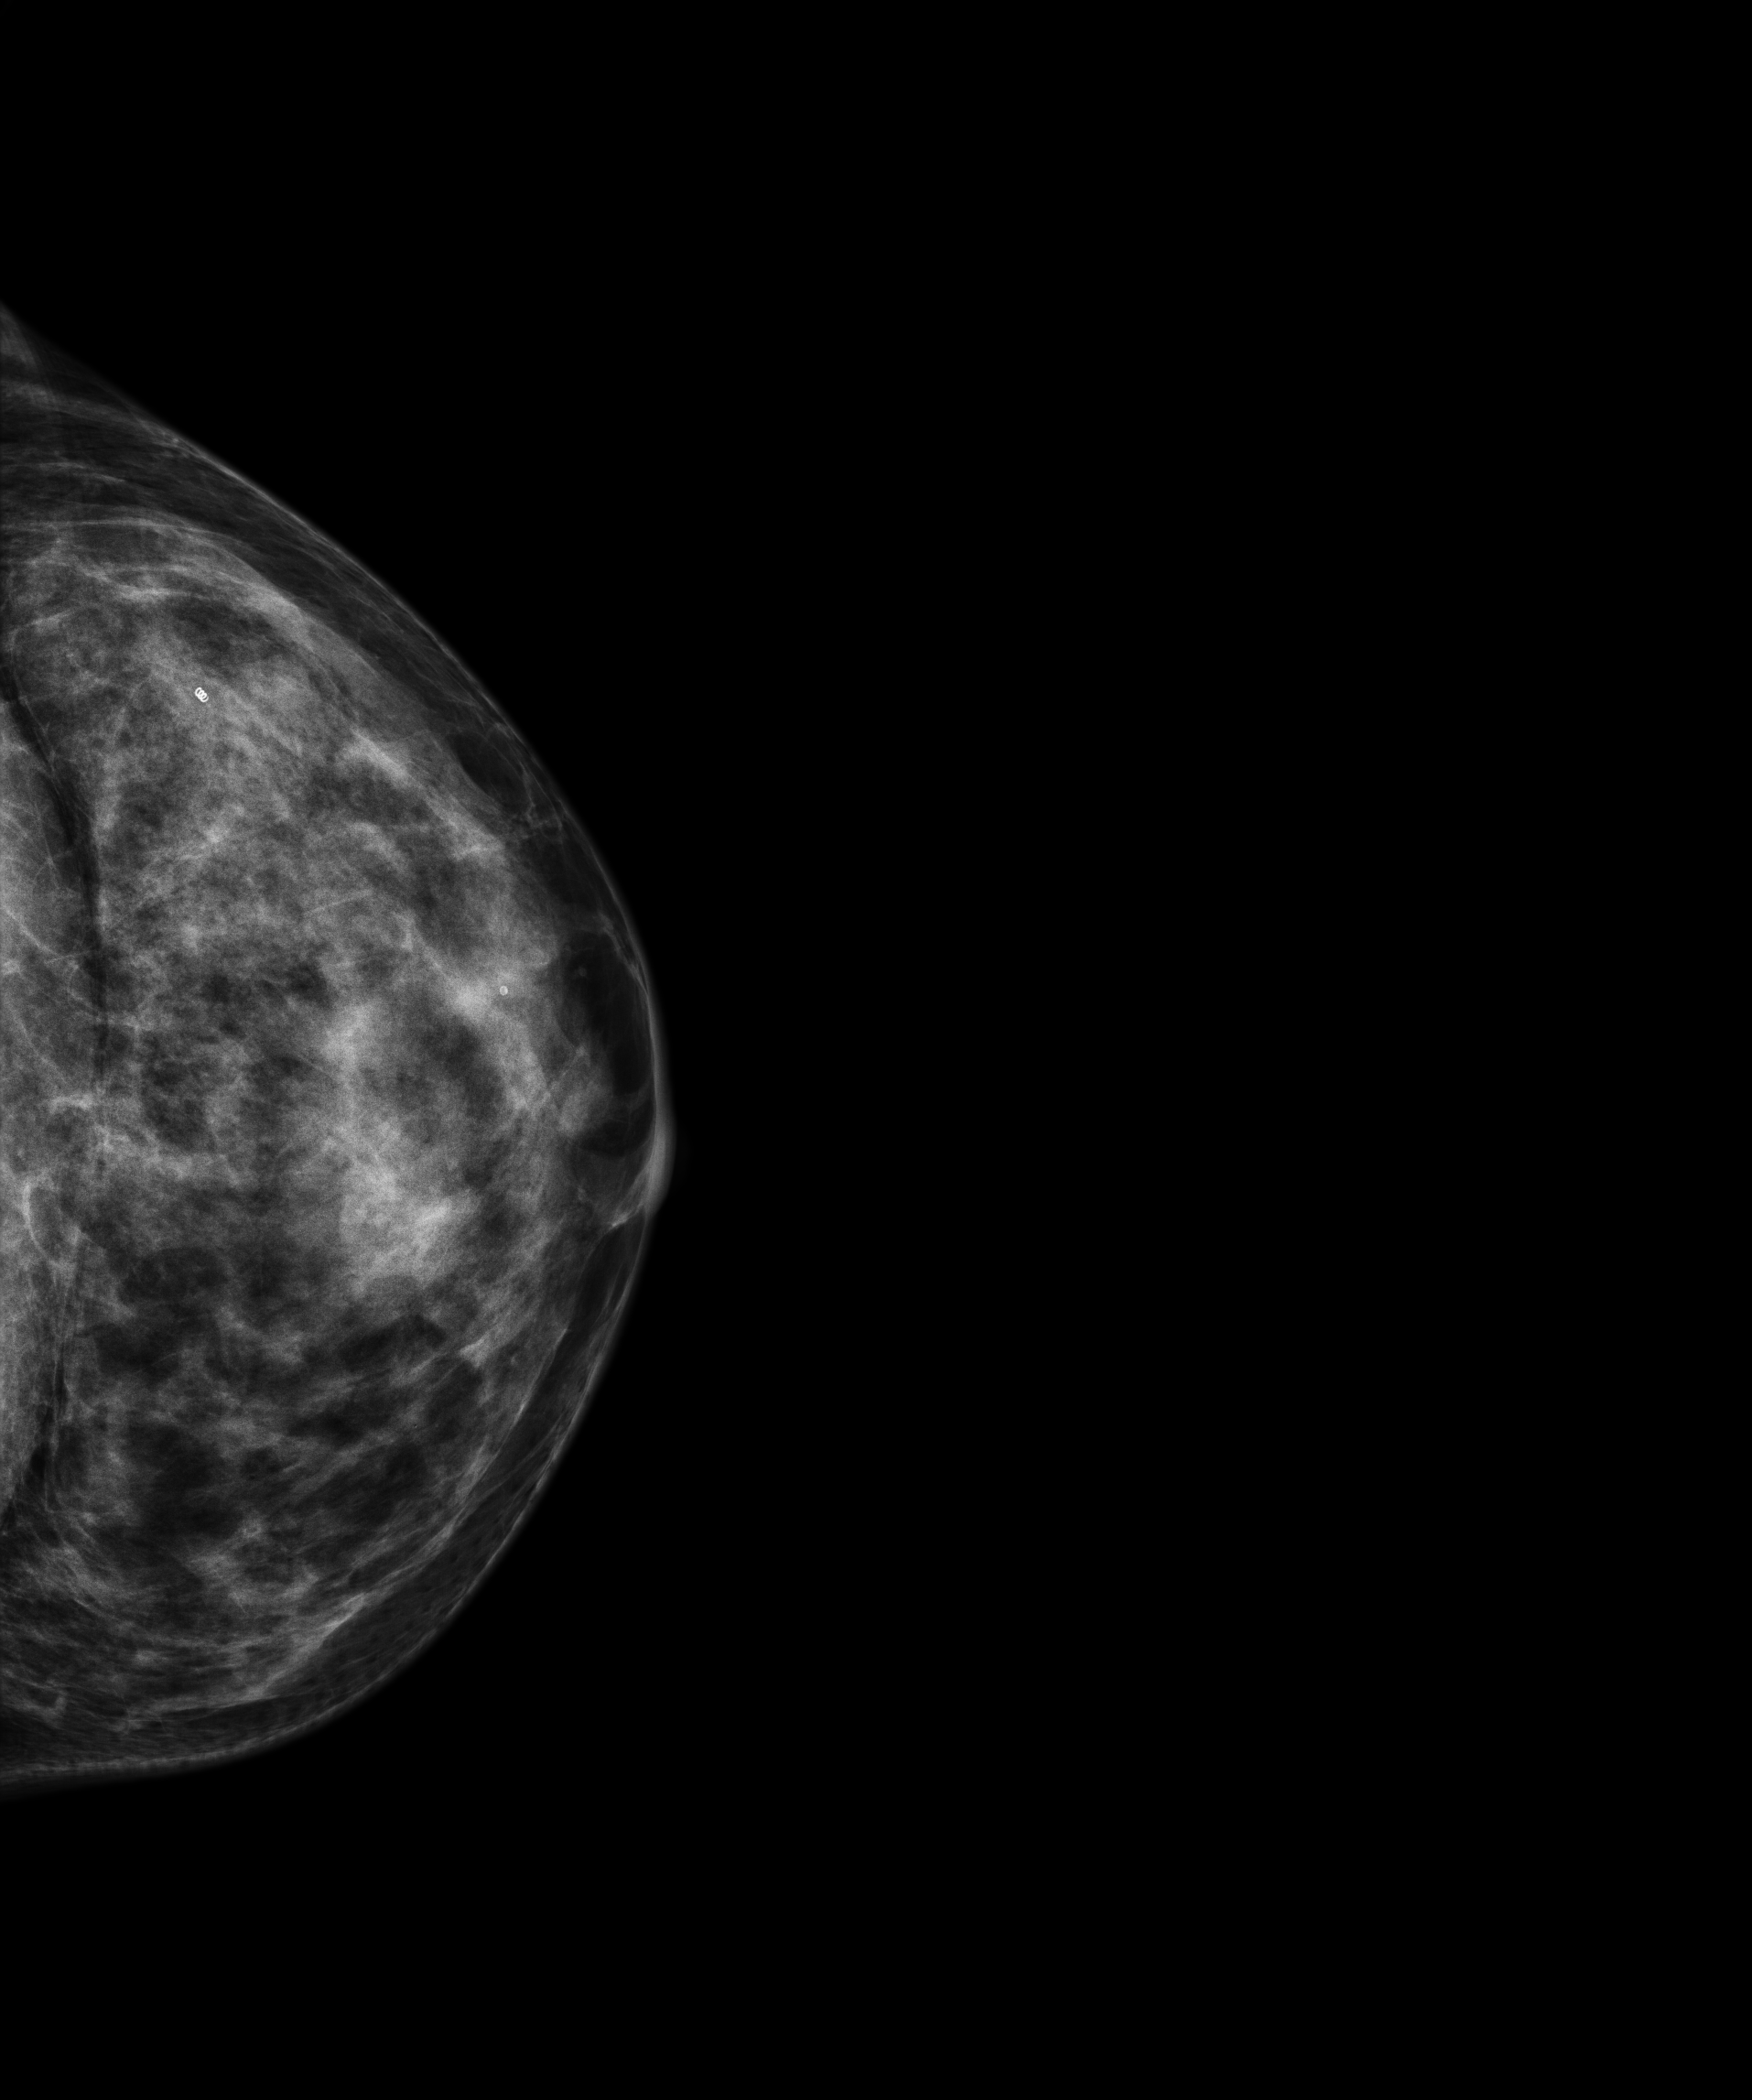
Full-field digital mammogram (FFDM), left breast, craniocaudal (CC) view, screening examination, compressed breast thickness 51 mm, system: Senographe Essential ADS_56.21.3. Patient aged 43 years (female).
Breast density at the screening exam (both breasts): extremely dense (BI-RADS density category d). Final BI-RADS category for the screening round (tomosynthesis exam, both breasts): category 2. Recall: no recall after this screen.